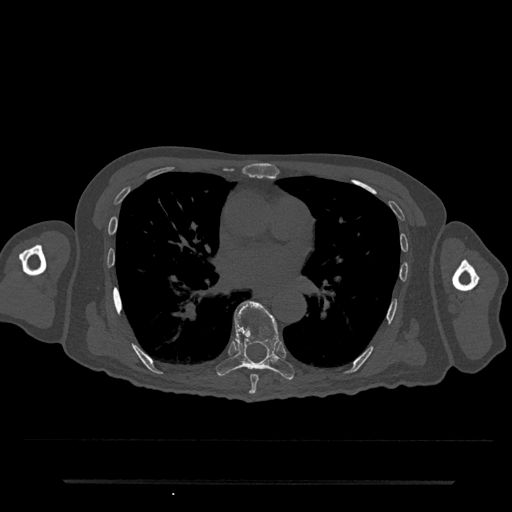
CT including the spine, one axial slice; slice 439 of 797 in the series (ordered by position); 120 kVp; bone window (W 1800 / L 400 HU); 0.5 mm slice thickness; 512 × 512 image matrix, field of view 427 × 427 mm. Patient: male, 74 years. From the clinical record (not read from this slice): primary cancer: prostate.
Annotated regions visible in this slice (semi-automatically segmented with operator editing):
- T7 vertebra: box from (x=249, y=374) to (x=259, y=395) px
- T8 vertebra: (x=216, y=301)–(x=295, y=381)